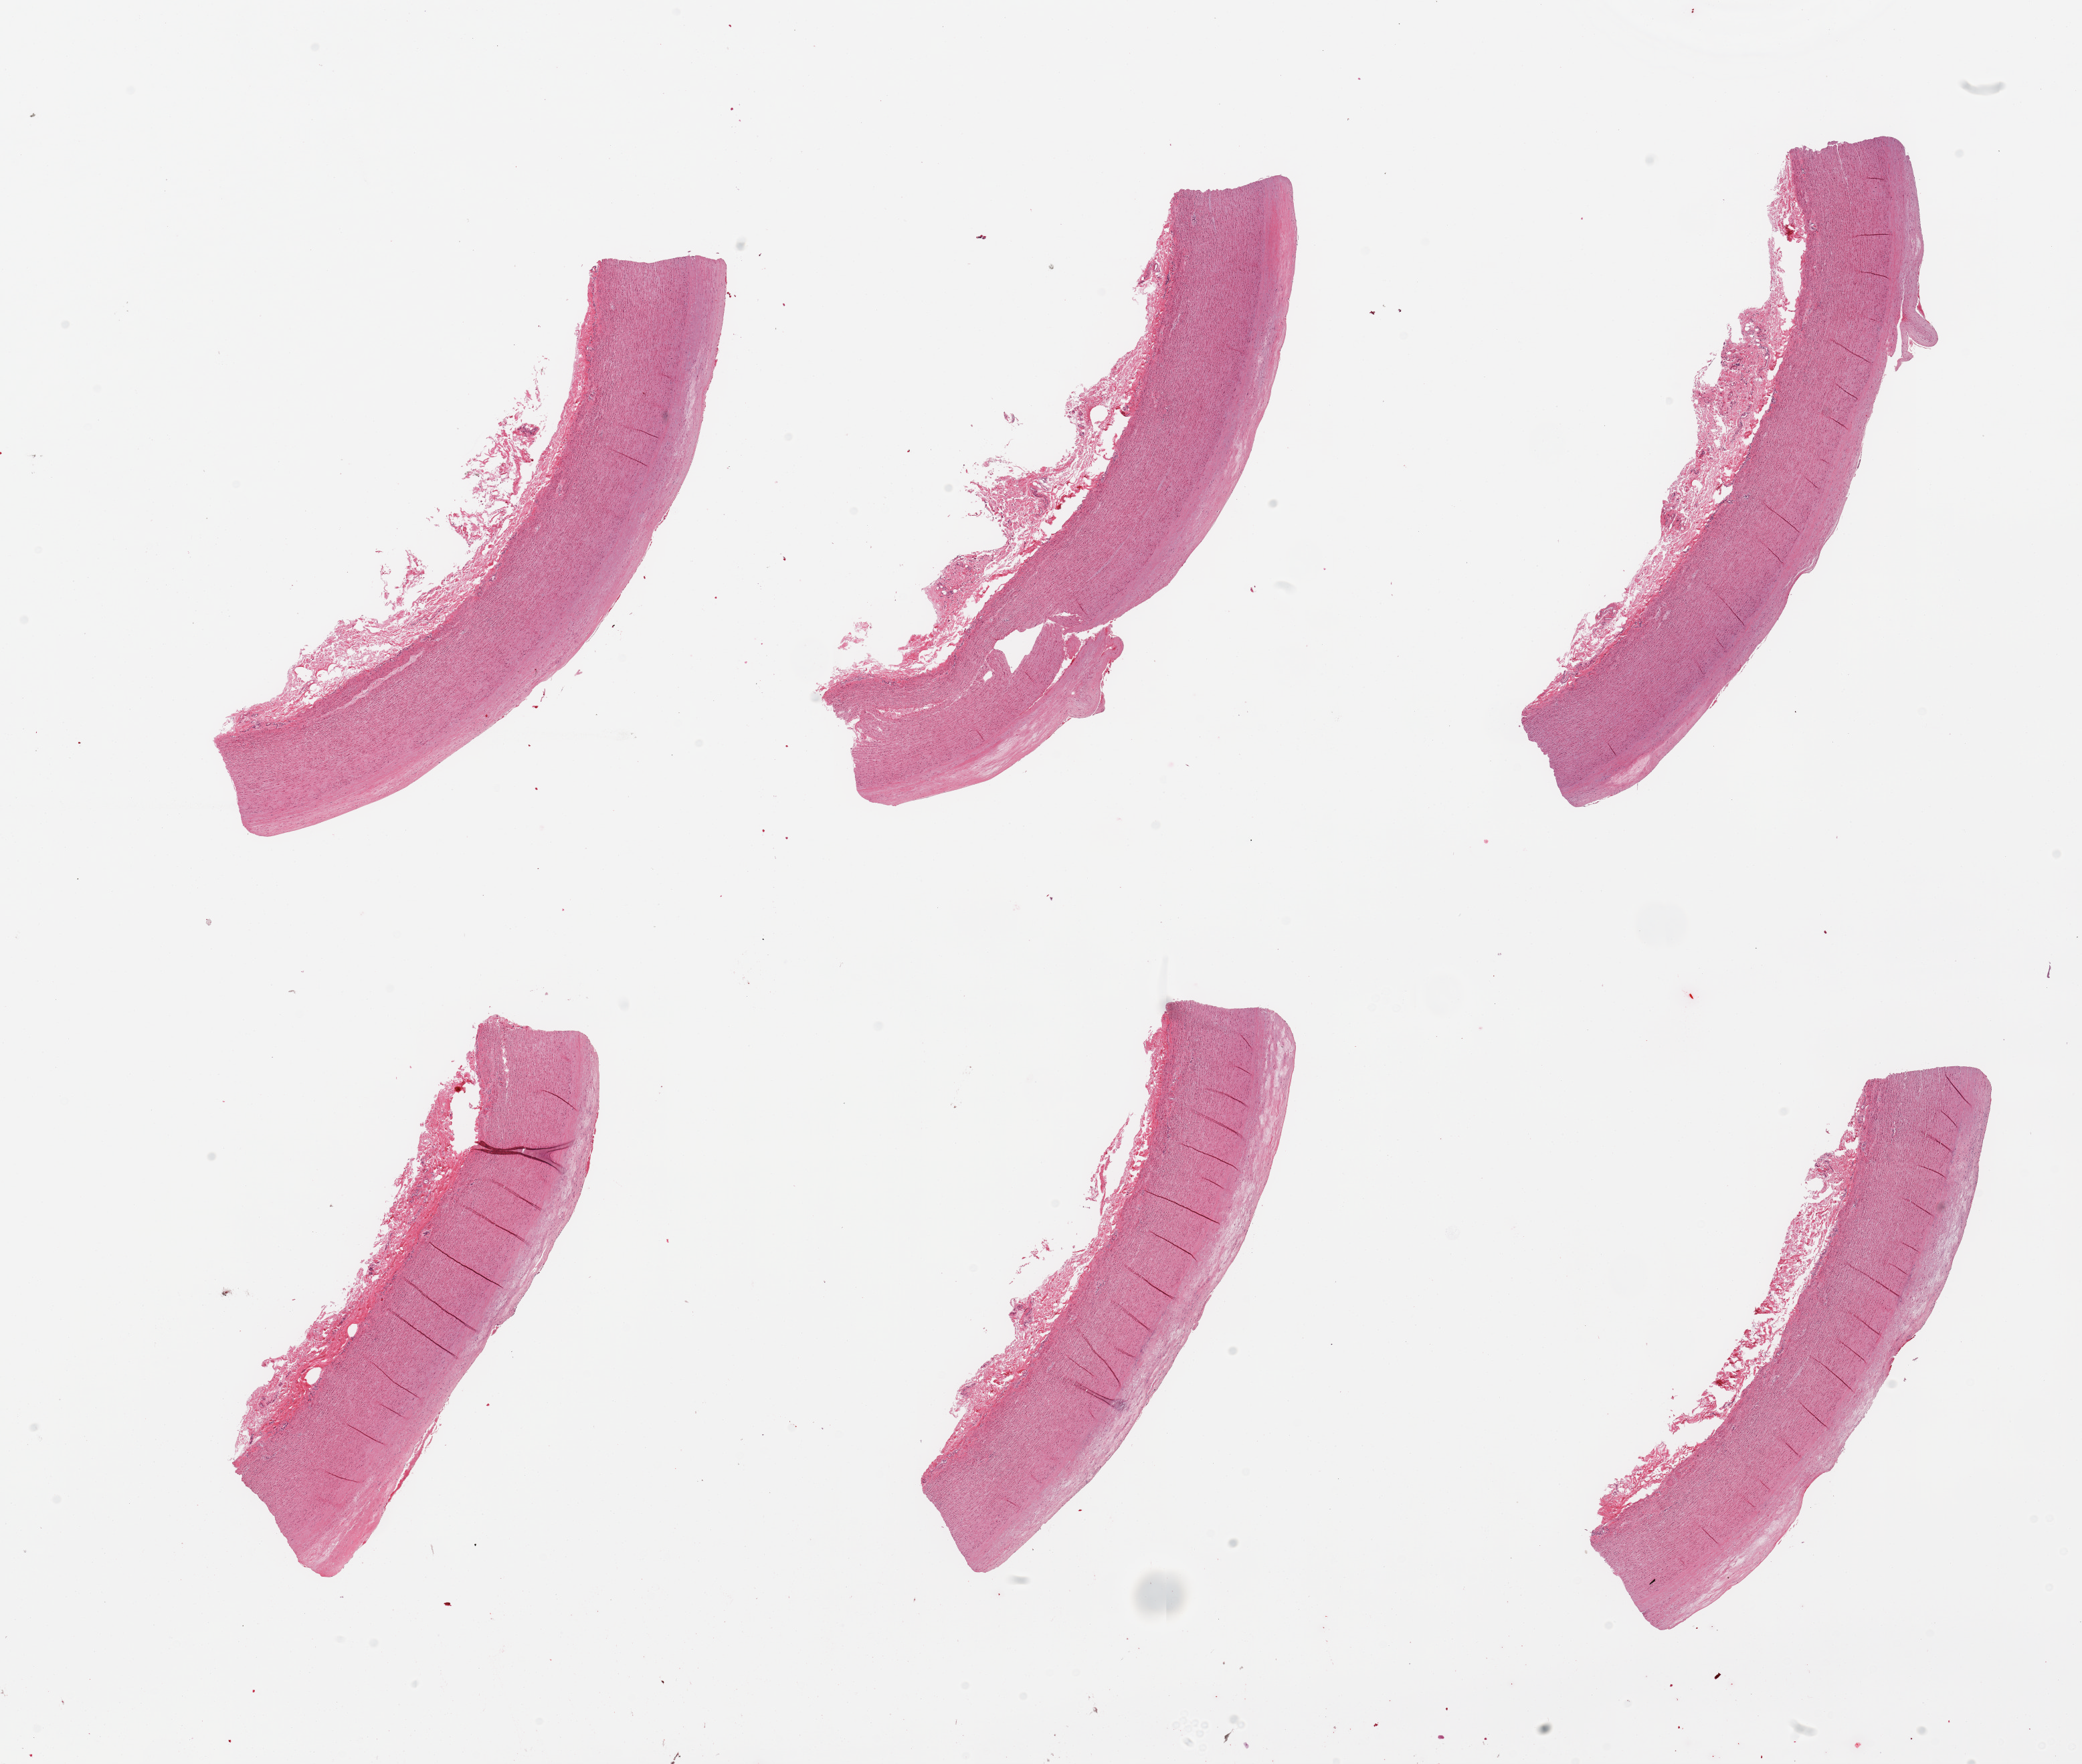
Whole-slide image, haematoxylin and eosin stain, brightfield — a low-resolution overview of the entire scanned area, about 24.6 x 20.9 mm (slide scanned at 20x); PAXgene-fixed paraffin-embedded (PFPE) section; sampled site (target tissue): aorta; tissue donor sample. Donor: male.
Review note (as recorded): 6 pieces; atherosclerosis.